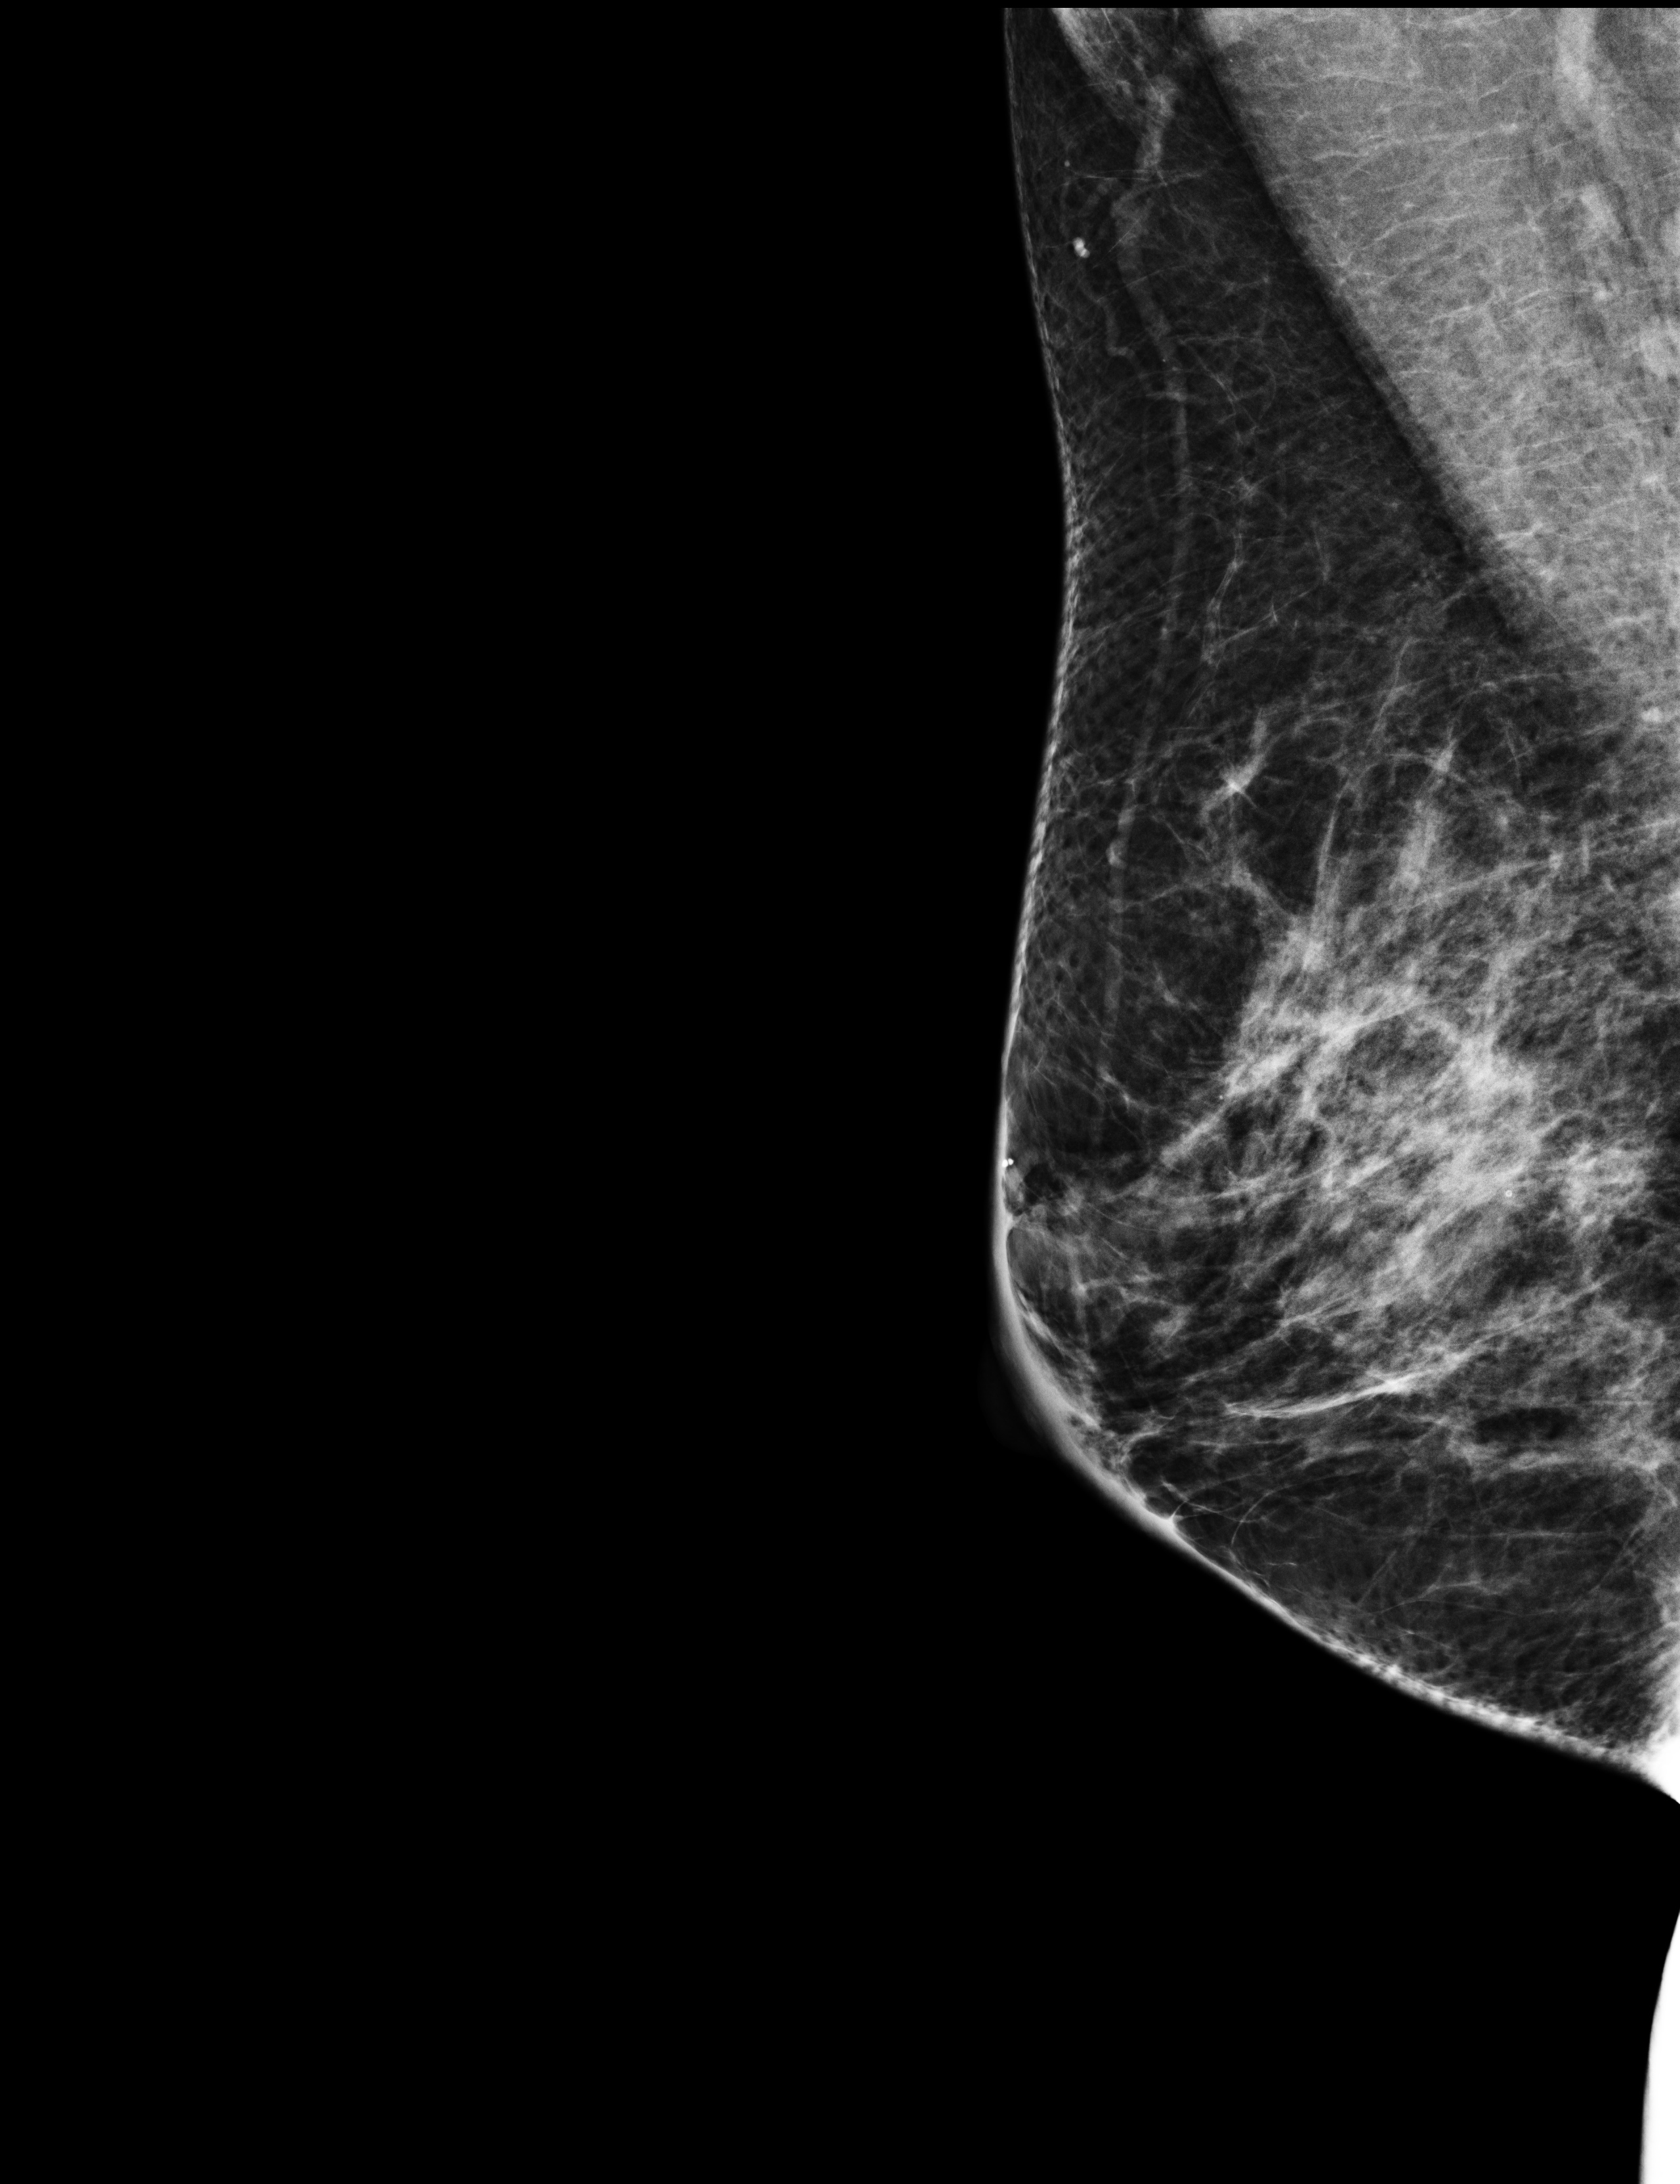
Full-field digital mammogram (FFDM), right breast, MLO view, screening examination, compressed breast thickness 69 mm, system: Selenia Dimensions. Female patient, age 43 years.
- BI-RADS breast density category at the screening exam (both breasts, scale 1–4): 3
- final BI-RADS assessment for this screening round (tomosynthesis exam, both breasts): category 1
- recall: no recall after this screen